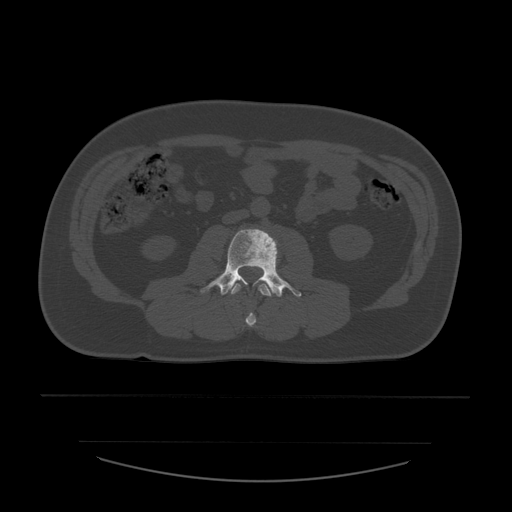
CT including the spine, one axial slice; slice 180 of 532 in the series (ordered by position); bone window (W 1800 / L 400 HU); 1.25 mm slice thickness; 512 × 512 image matrix, field of view 441 × 441 mm. Patient age 44 years. From the clinical record (not read from this slice): primary cancer: soft tissue sarcoma.
Outlined on this slice (semi-automatically segmented with operator editing):
- L2 vertebra: bounding box [x1, y1, x2, y2] px = [231, 283, 273, 328]
- L3 vertebra: [201, 229, 302, 297]